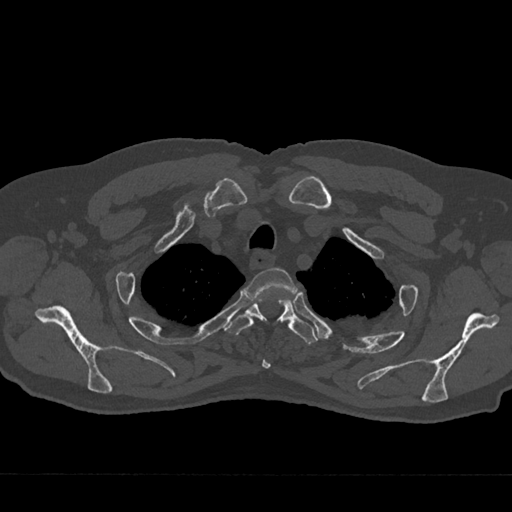
CT including the spine, one axial slice. Position 586 of 797 along the scan axis. Reconstruction kernel Br40s/3. 120 kVp. Bone window (W 1800 / L 400 HU). 0.5 mm slice thickness. 512 × 512 image matrix, field of view 377 × 377 mm. Male patient, age 75 years. From the clinical record (not read from this slice): primary cancer: renal; vertebrae with lytic lesions (as recorded): T4.
Outlined on this slice (semi-automatic segmentation, software-assisted and operator-edited):
- T2 vertebra: bounding box [x1, y1, x2, y2] px = [248, 268, 297, 369]
- T3 vertebra: [226, 297, 318, 345]